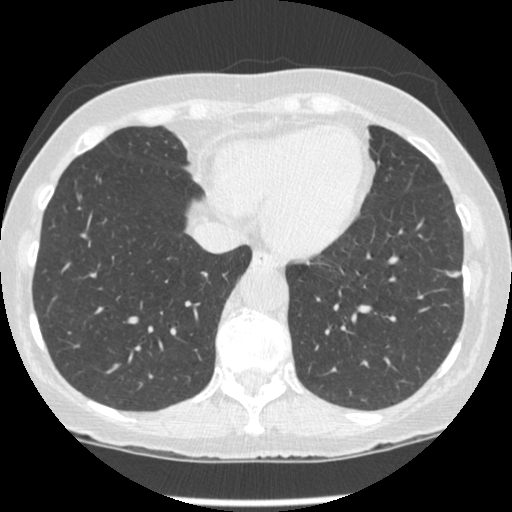
Low-dose screening chest CT, one axial slice; 120 kVp; lung window (W 1500 / L -600 HU); 1.25 mm slice thickness; 512 × 512 image matrix, field of view 303 × 303 mm.
Structures marked on this image (manually delineated by an expert):
- lesion 1 (tumor, lower lobe of left lung): bounding box <447,271,459,277> (left, top, right, bottom; pixels)